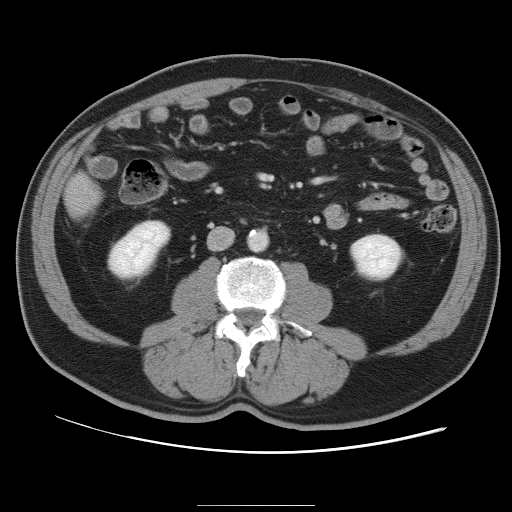
Contrast-enhanced abdominal CT, one axial slice. Position 21 of 105 along the scan axis. 120 kVp. Intravenous contrast given. Soft-tissue window (W 400 / L 40 HU). 5 mm slice thickness. 512 × 512 image matrix. Male patient, age 64 years. Case-level facts recorded for this patient, not image findings: diagnosis: colorectal cancer liver metastases, imaged before liver resection.
Outlined on this slice (manually delineated by an expert):
- liver: bounding box (x1, y1, x2, y2) in pixels: (67, 175, 96, 213)
- planned liver remnant (the part of the liver to remain after resection): (67, 175, 96, 214)